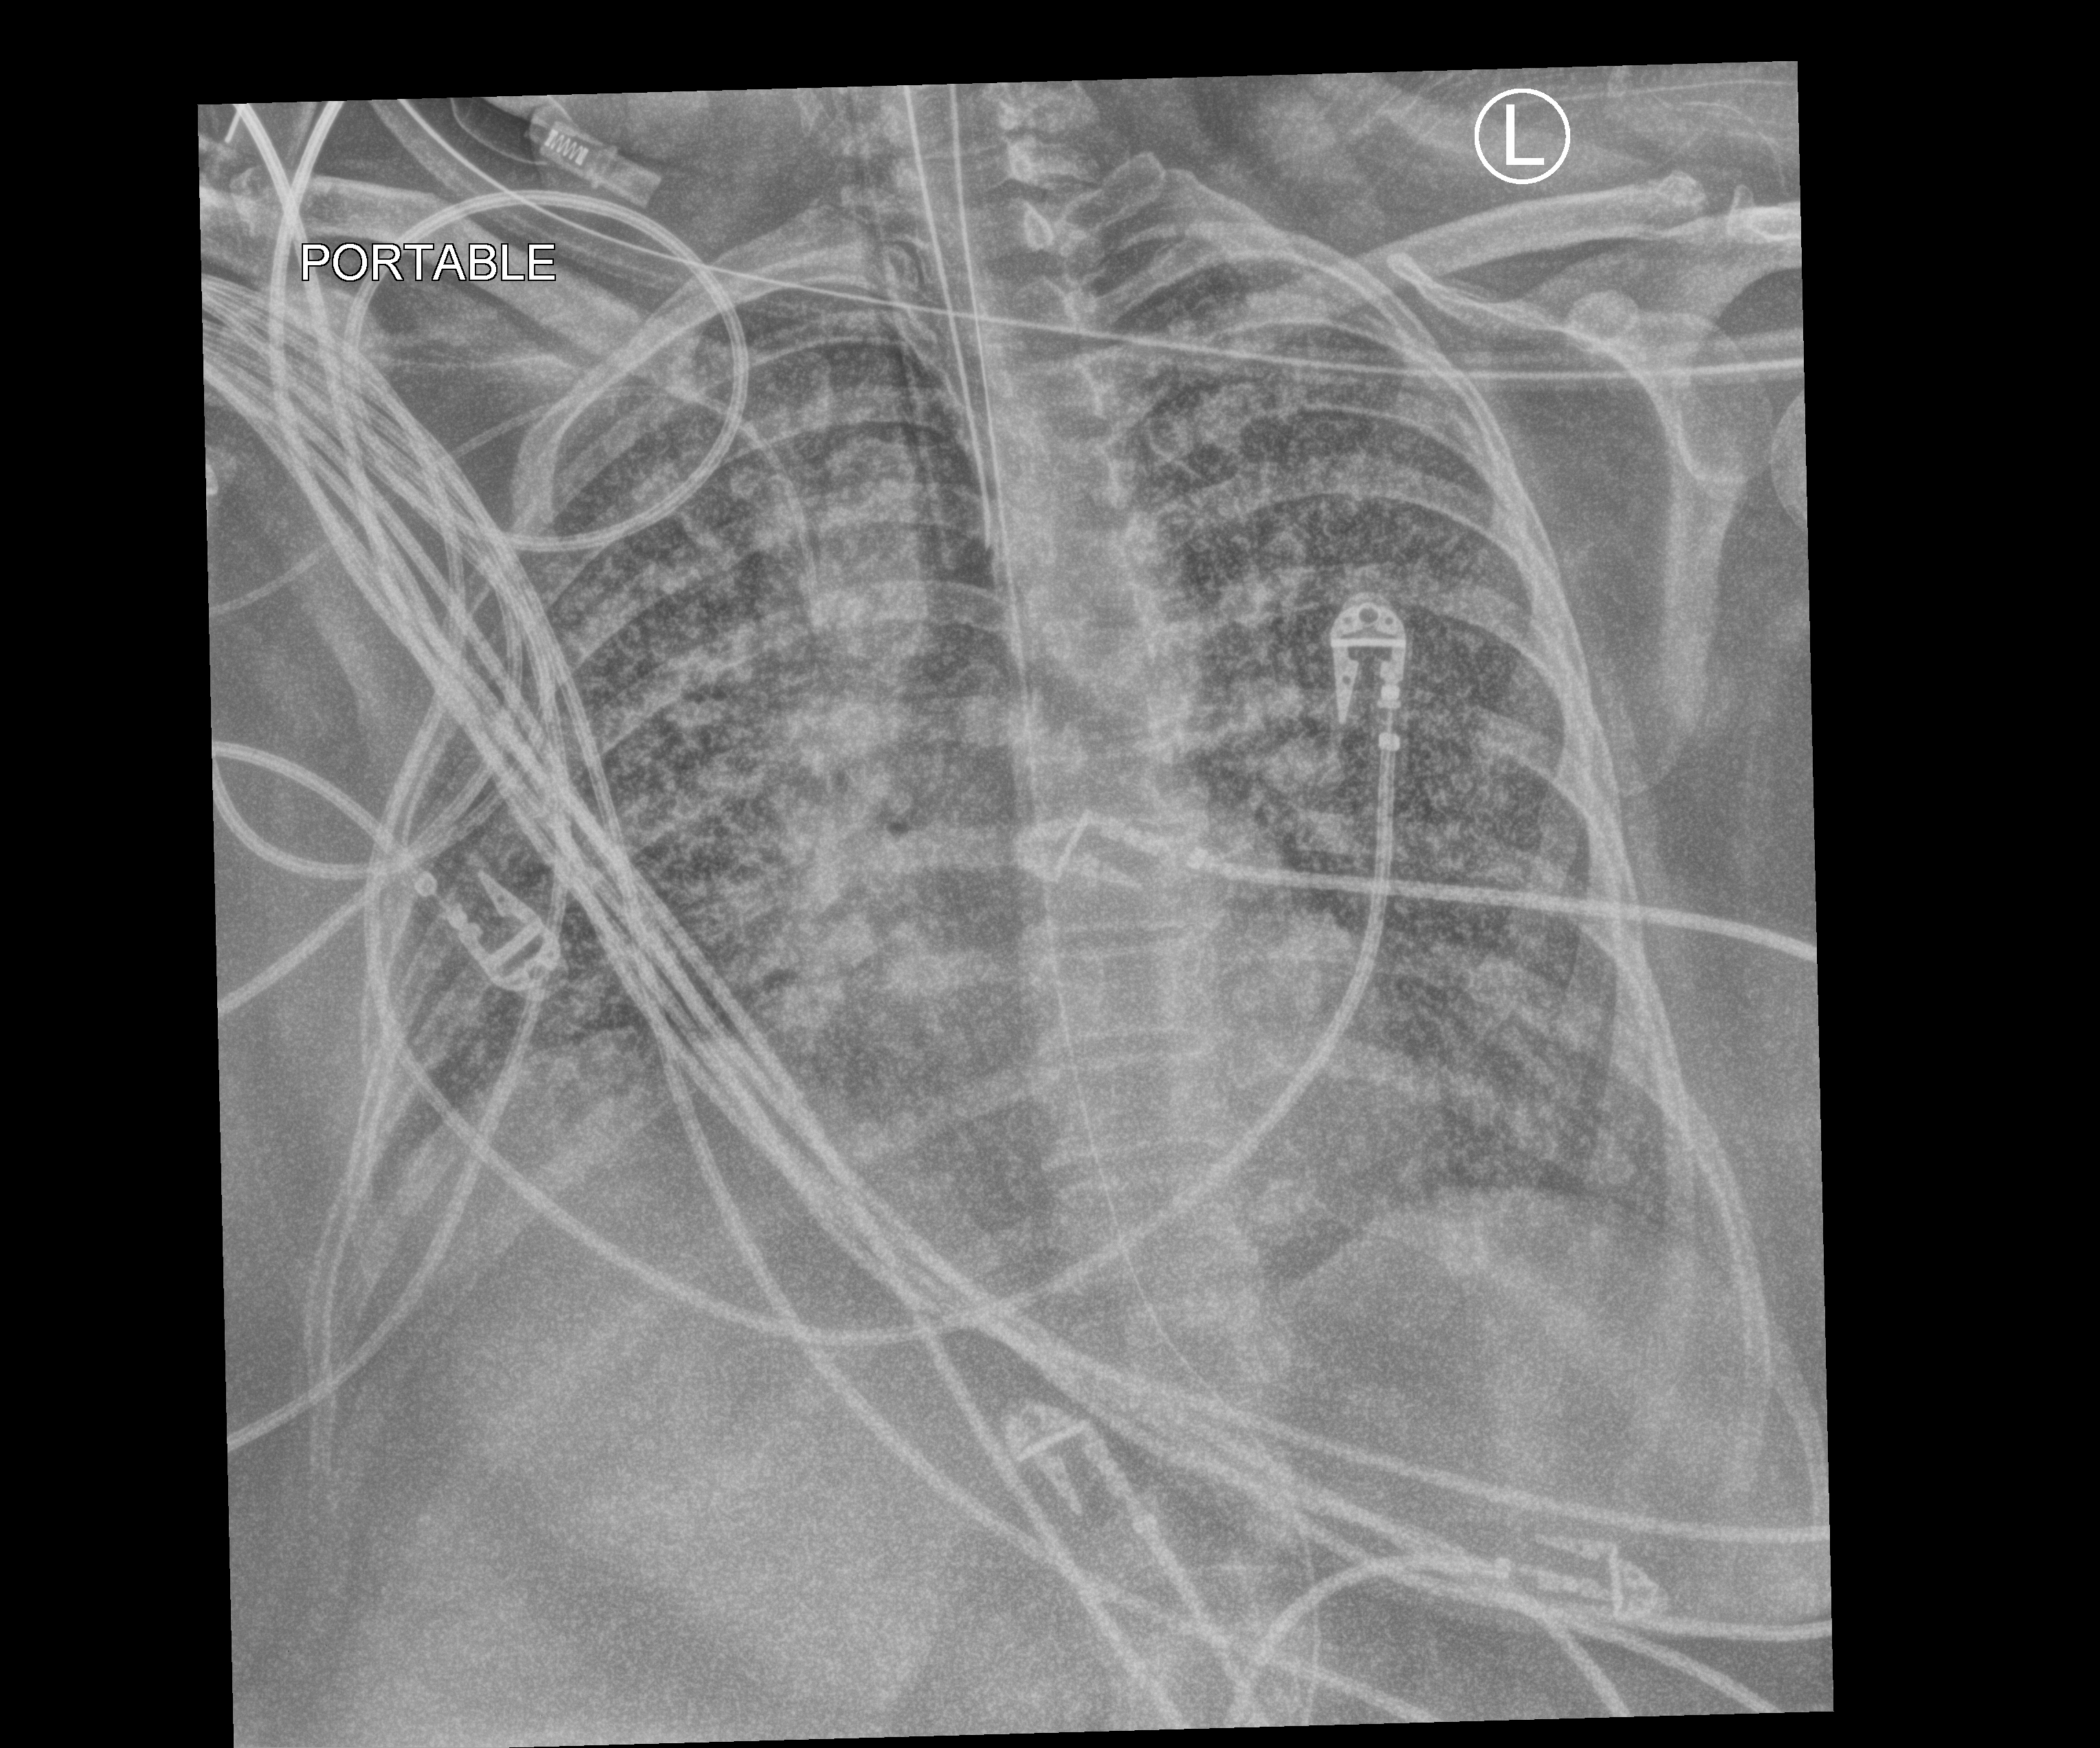
Chest X-ray (portable); anteroposterior (AP) projection. Patient hospitalised with COVID-19; female, aged 18–59 years.
From the hospital-stay record, not from the radiograph (when in the stay this image was taken is not recorded): COPD (admission record): no; admitted to intensive care during this hospital stay: yes; mechanically ventilated during this hospital stay: yes.